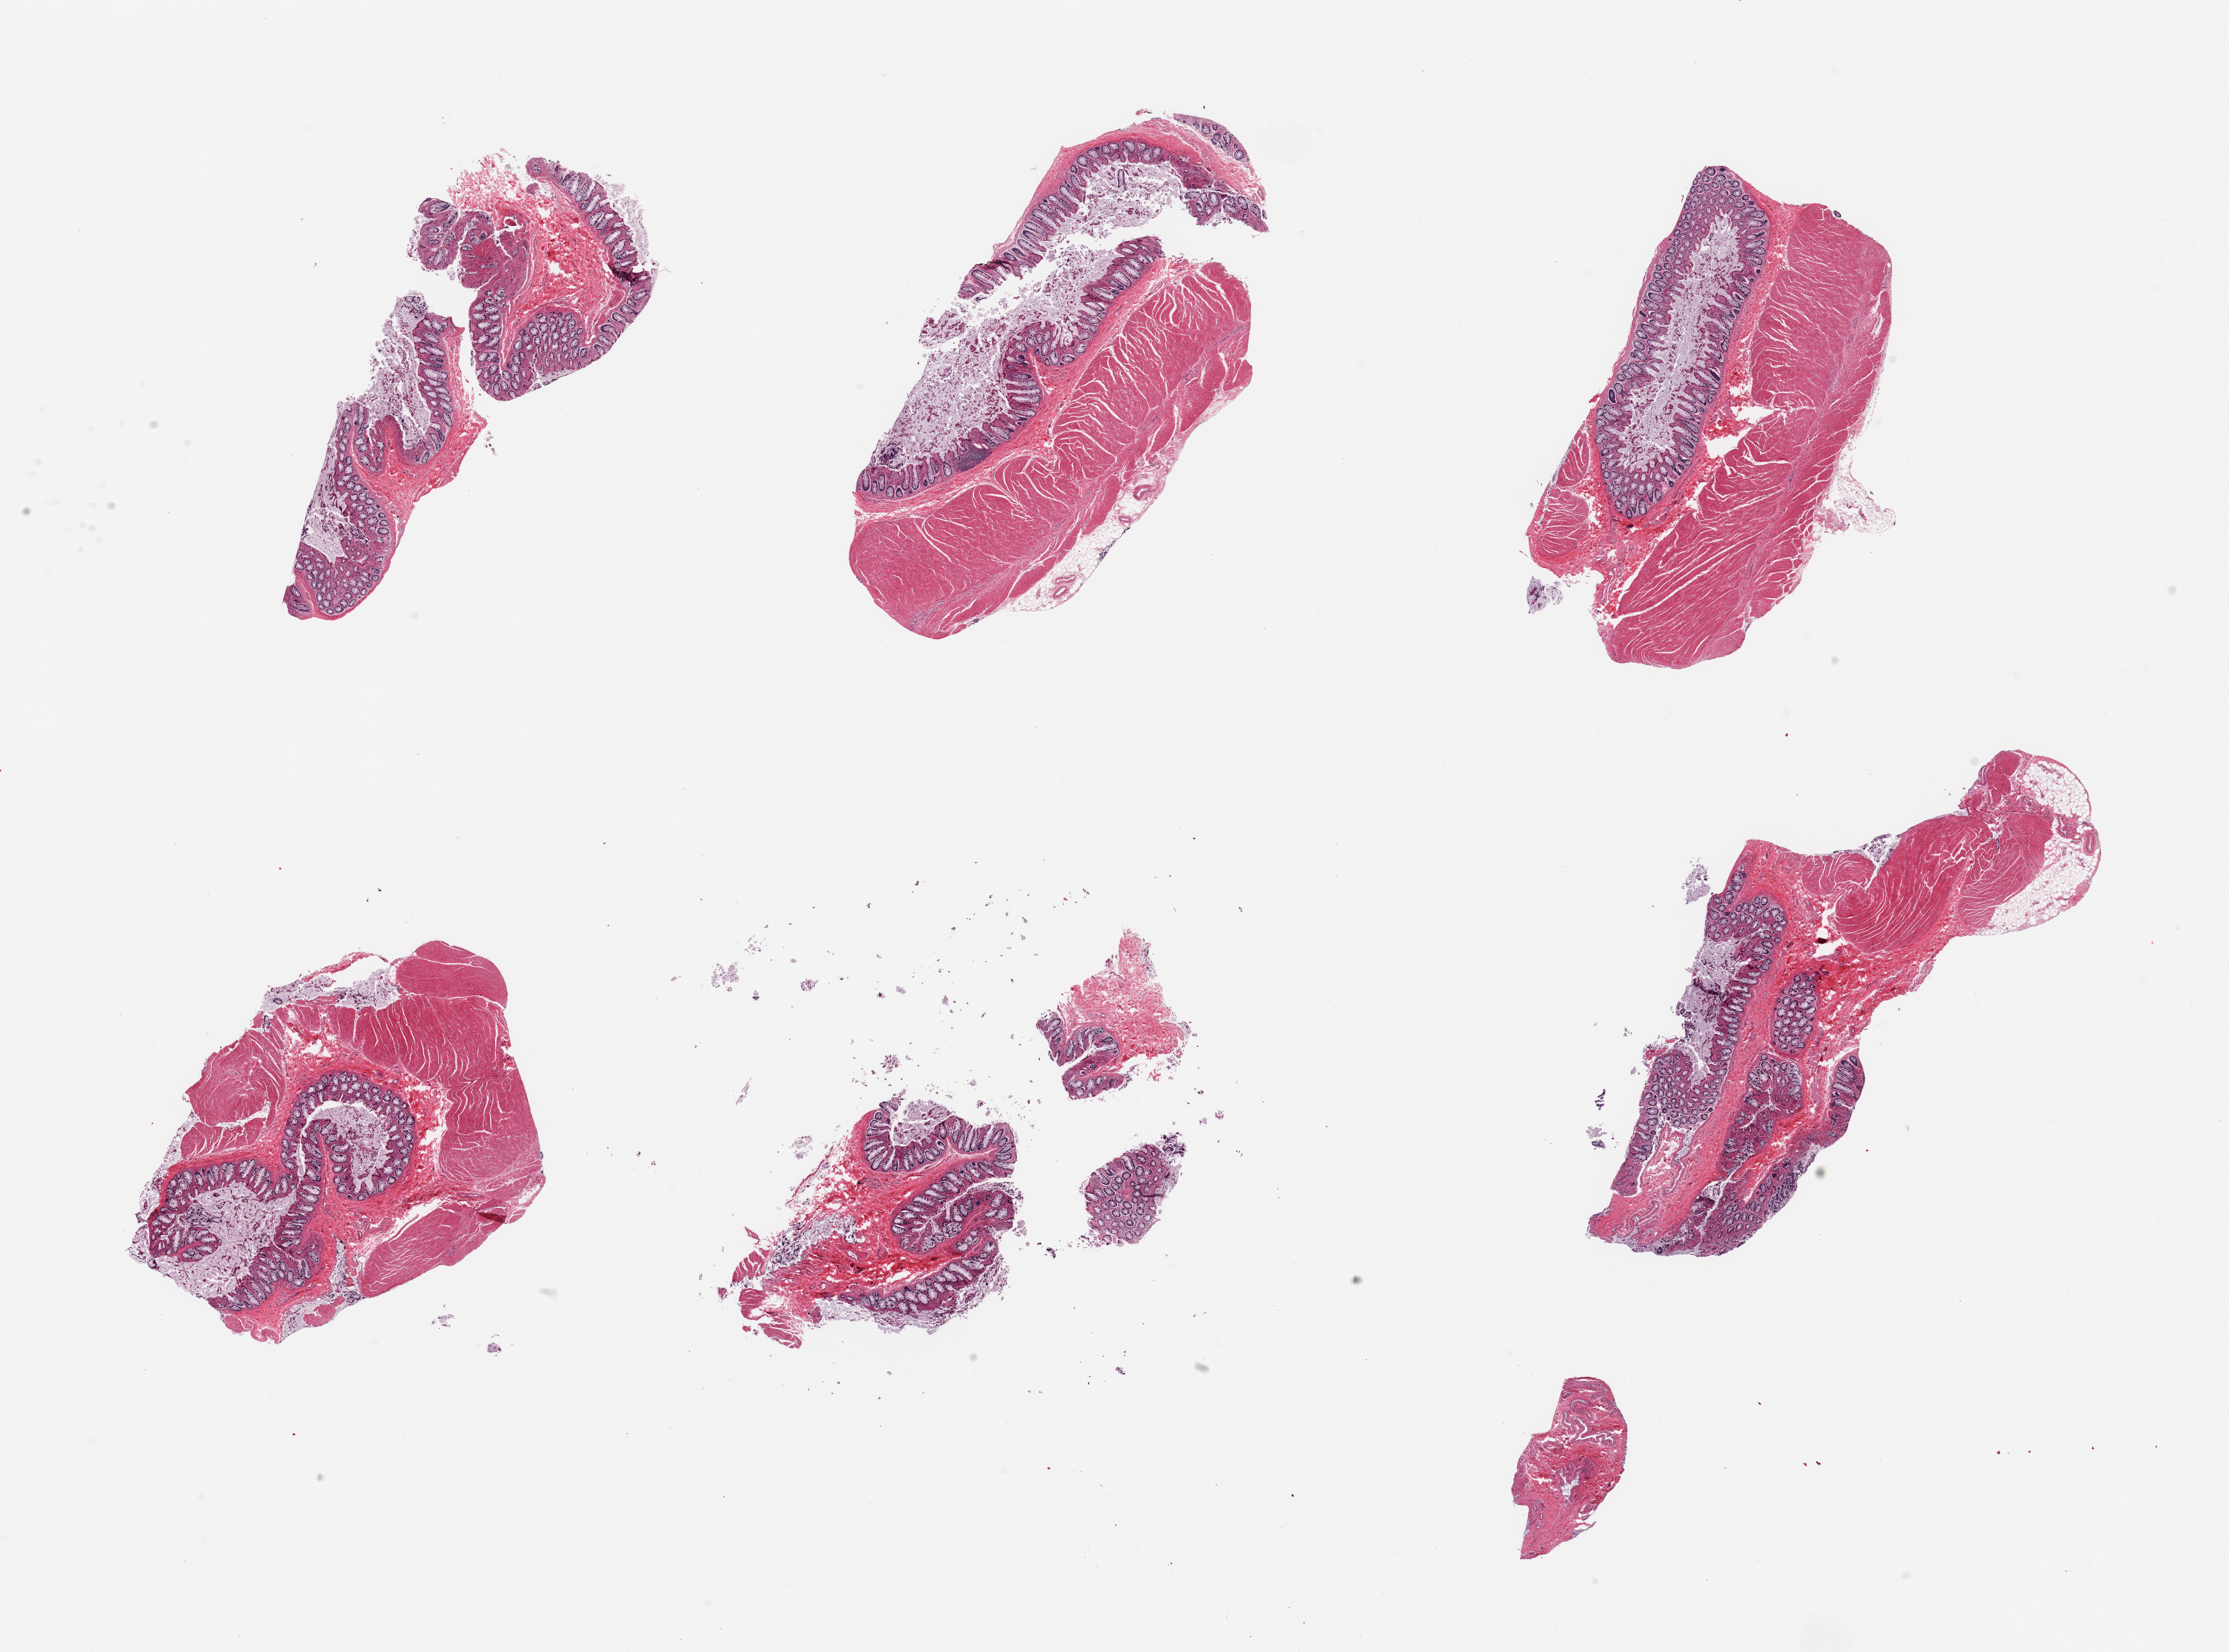
Hematoxylin and eosin (H&E) whole-slide image, brightfield — a low-resolution overview of the entire scanned area, about 27.6 x 20.4 mm, PAXgene-fixed paraffin-embedded (PFPE) section, sampled site (target tissue): sigmoid colon, donor tissue sample. Donor sex: female.
* reviewer comment on this tissue sample: 6 pieces; muscularis (target) and mucosa (not target)